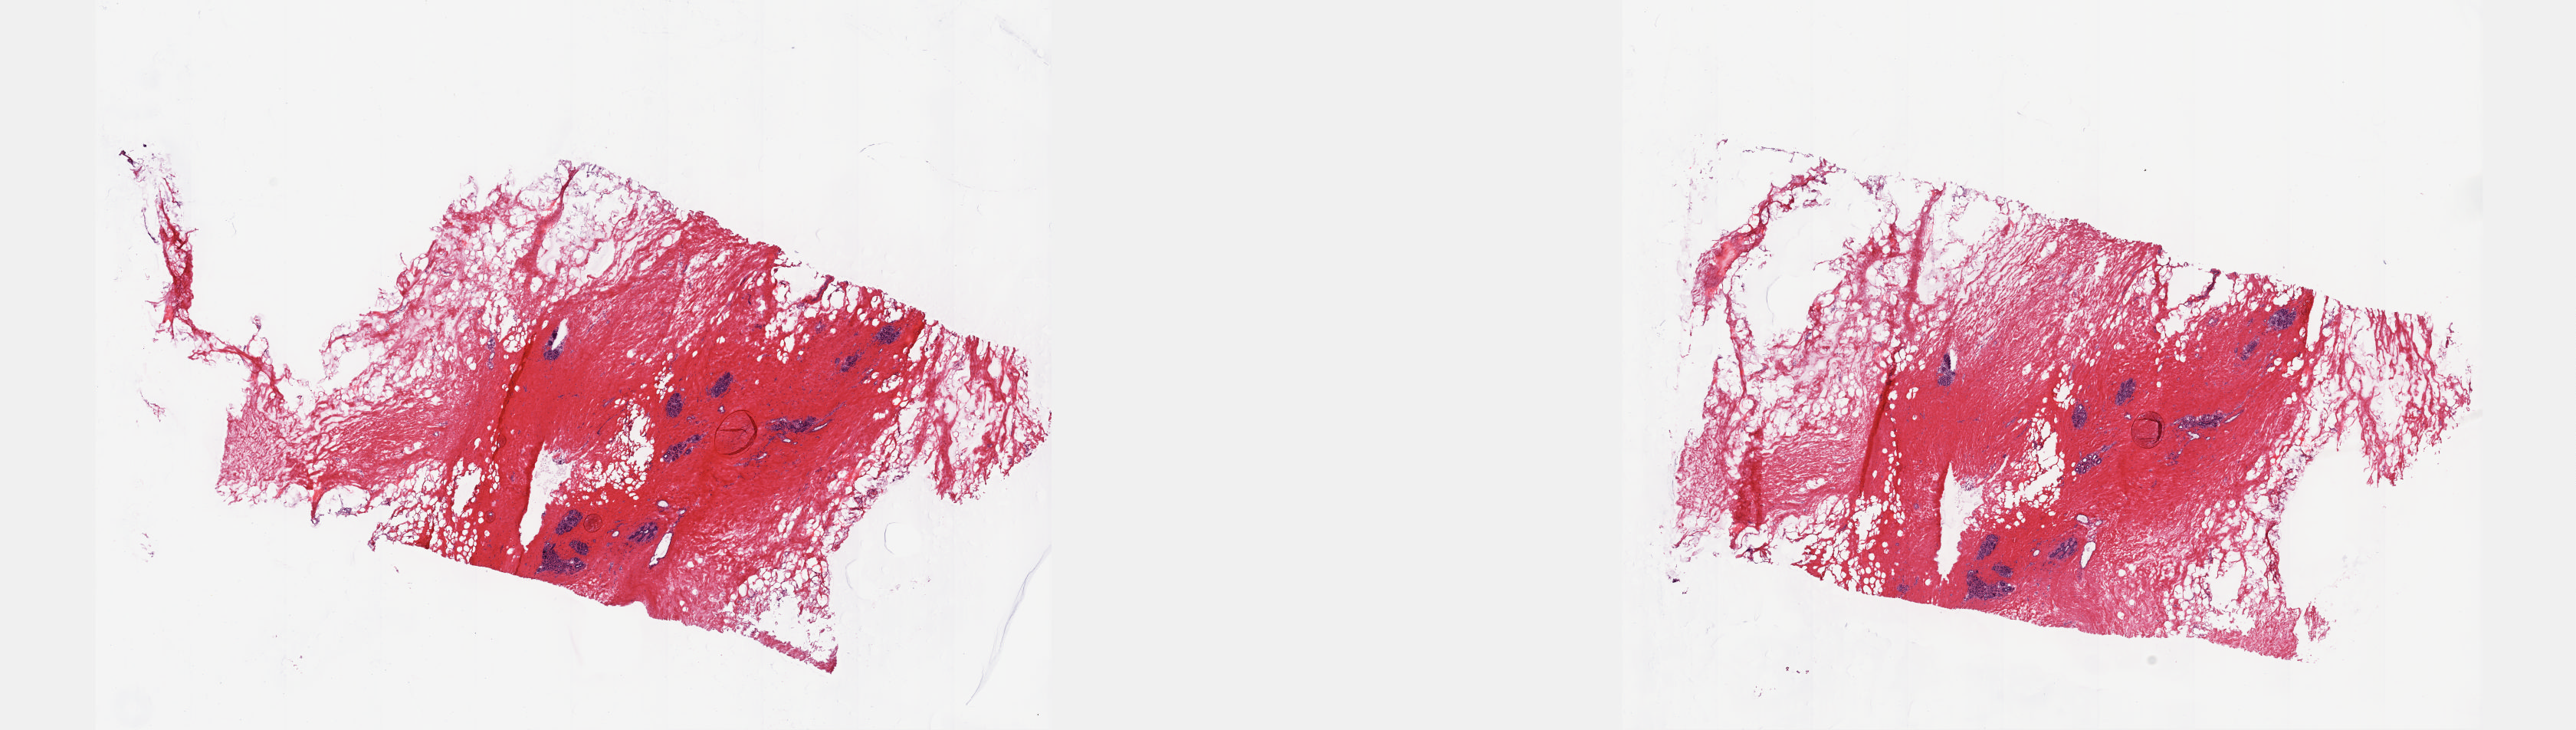
Digitized H&E-stained tissue section (whole slide), low-resolution overview of the scanned area, about 27.1 x 7.7 mm (acquisition: 20x scan). Frozen section from the top of the tissue portion. Sample: solid tissue normal (non-tumour tissue), breast. Female, age 46 years at initial diagnosis. Slide review estimates, as recorded: tumour cells 0%, tumour nuclei 0%, normal cells 100%, stromal cells 0%, necrosis 0%. Inflammatory infiltration, as recorded: lymphocyte infiltration 1%, monocyte infiltration 0%, neutrophil infiltration 0%.
This section: solid tissue normal sample (biorepository sample class). Patient diagnosis: Lobular carcinoma, NOS.